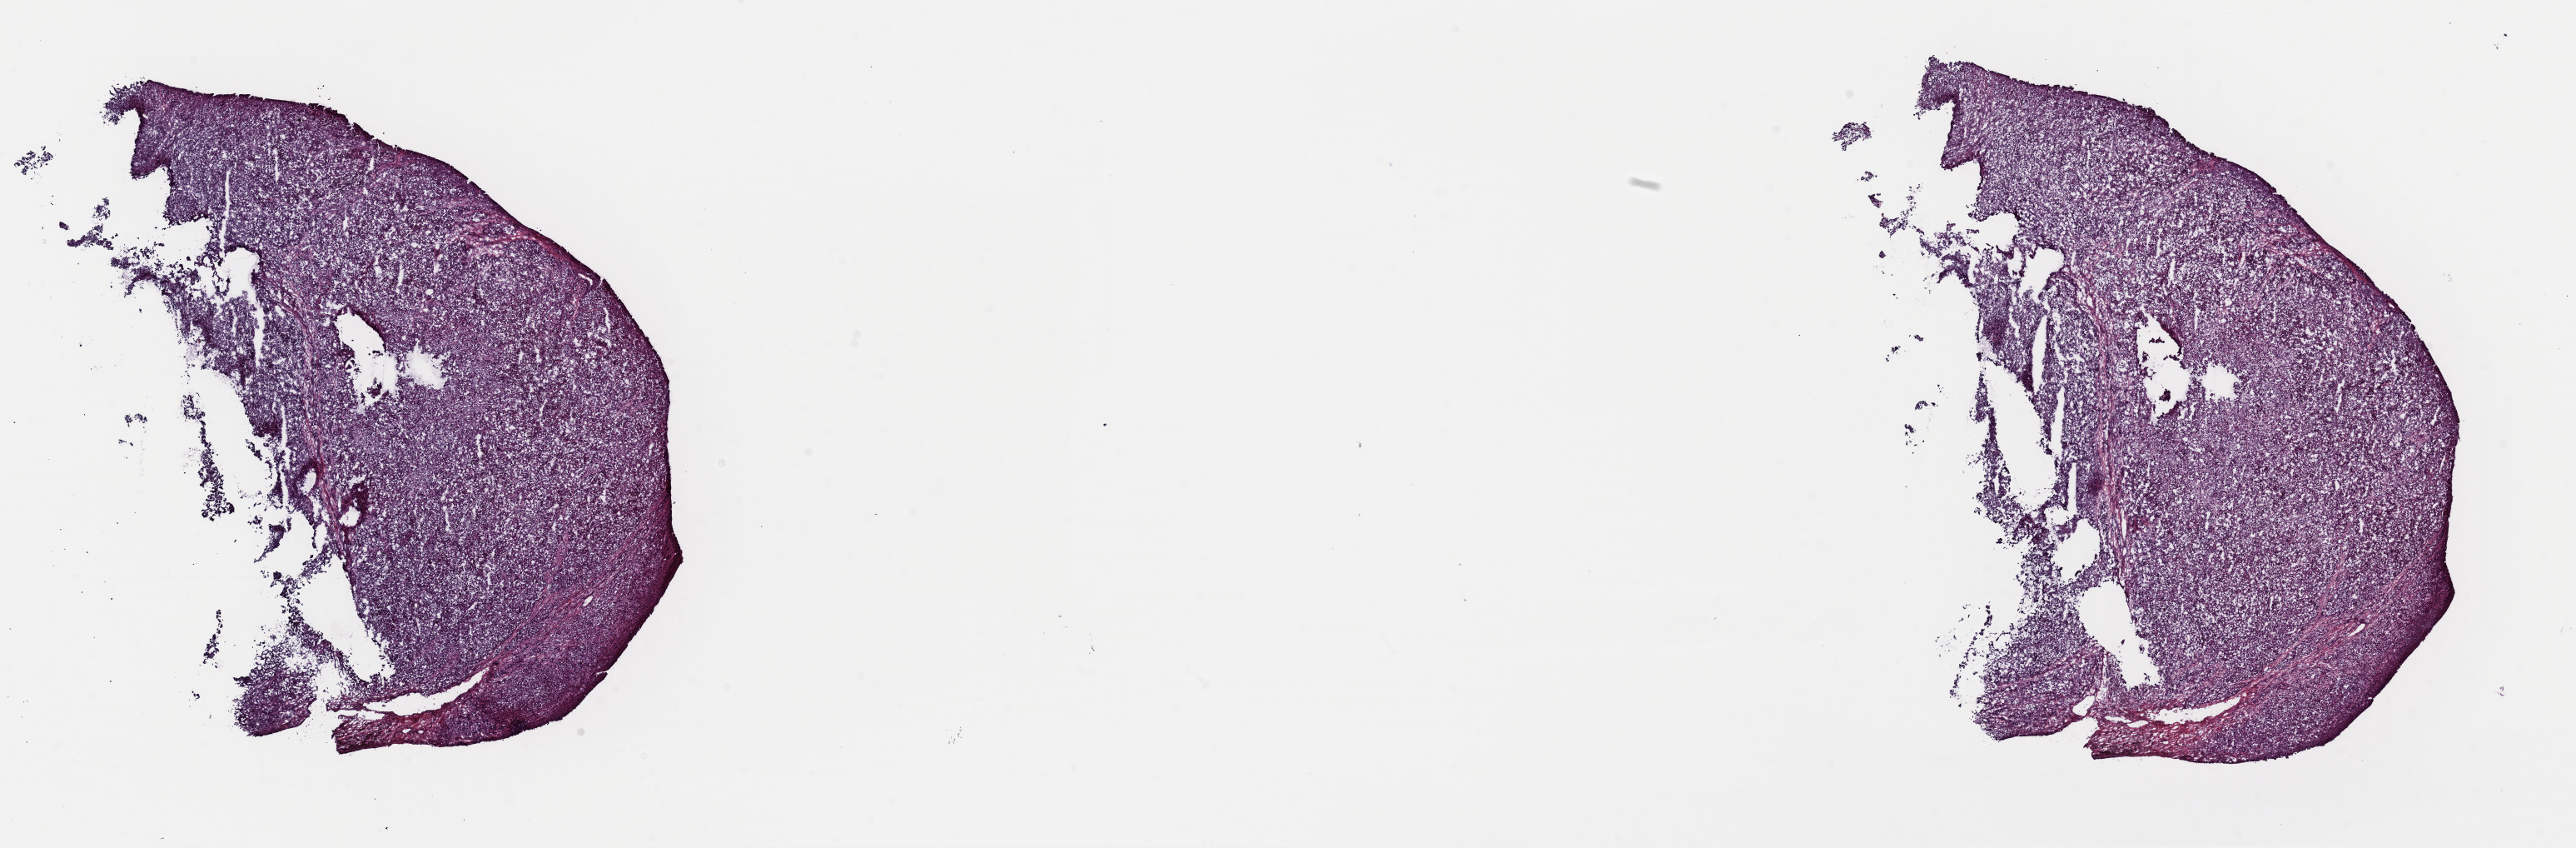
Hematoxylin and eosin (H&E) stained whole-slide image — whole scanned area (about 24.4 x 8.0 mm, from a 40x scan) shown as a low-resolution overview. Frozen section from the top of the tissue portion. Metastatic tumour sample. Patient: male, age at initial diagnosis 61 years. Composition of this section per pathologist review: tumour cells 100%, tumour nuclei 95%, normal cells 0%, stromal cells 0%, necrosis 0%. Infiltration values recorded for this section: lymphocyte infiltration 0%, monocyte infiltration 0%, neutrophil infiltration 0%.
This section: metastatic tumour tissue. Patient diagnosis: Malignant melanoma, NOS.